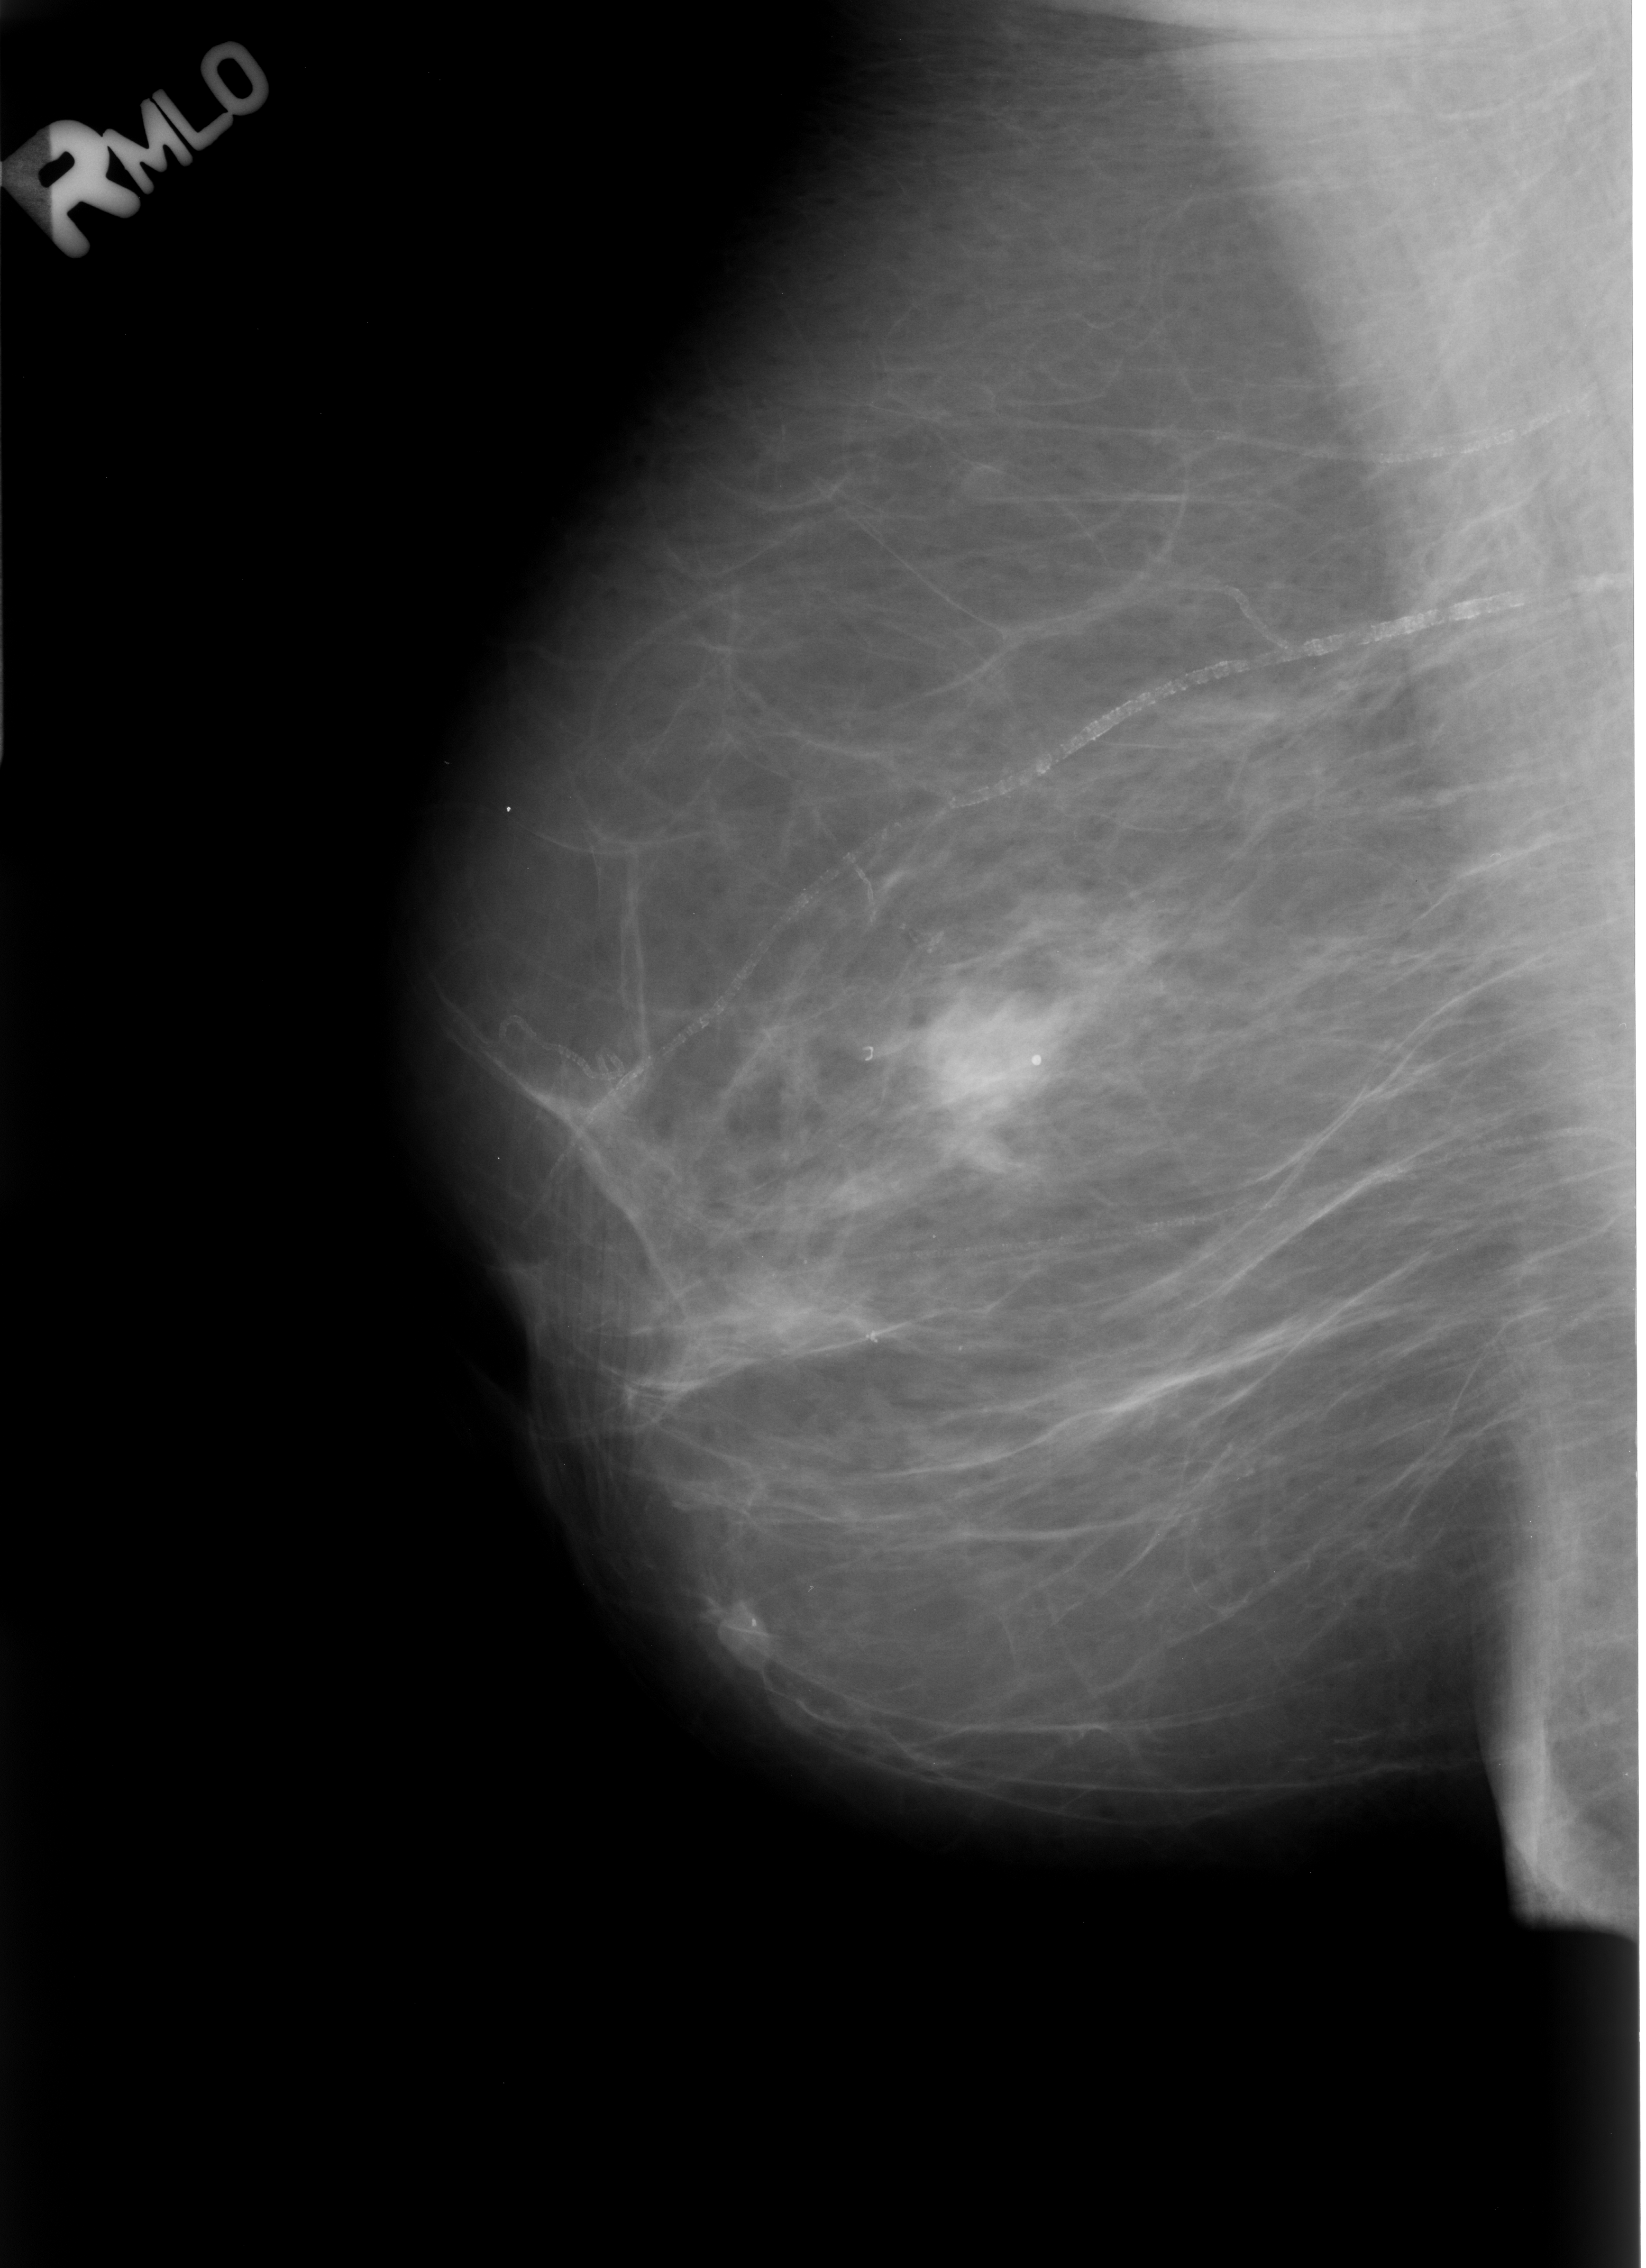
Scanned film-screen mammogram; right breast; mediolateral oblique (MLO) view; BI-RADS breast density category 2 (scale 1–4); 1646 × 2268 image matrix.
Expert-marked regions of interest on this film, with their recorded descriptors:
- Finding 1 of 2: calcifications, morphology vascular; BI-RADS assessment category 2; subtlety rating 5 on a 1 (subtle) to 5 (obvious) scale; outcome (as recorded, no biopsy): benign without callback (not worked up further): bounding box [x1, y1, x2, y2] px = [495, 550, 1634, 1203]
- Finding 2 of 2: calcifications, morphology round and regular; BI-RADS assessment category 2; subtlety rating 5 on a 1 (subtle) to 5 (obvious) scale; benign; no additional work-up was recommended (outcome (as recorded, no biopsy): benign without callback): [1011, 1032, 1063, 1097]